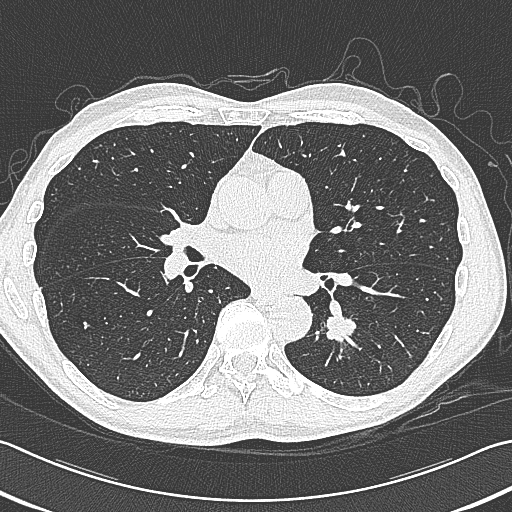
Chest CT (low-dose screening protocol), one axial image. First (baseline) screen. Lung window (W 1500 / L -600 HU). 1 mm slice thickness. Lung (sharp) reconstruction kernel (B80f). 120 kVp. Male participant, aged 59 years at enrolment.
Expert-annotated lung lesion, bounding box <313,295,376,353> (left, top, right, bottom; pixels). Reader record for this screening exam (exam-level; its link to the box is not recorded): non-calcified nodule or mass ≥4 mm, left lower lobe, 15 × 15 mm, smooth margins, soft tissue attenuation. Official screen result: positive, change unspecified: nodule(s) >= 4 mm or enlarging nodule(s), mass(es), or other non-specific abnormalities suspicious for lung cancer. Participant outcome: lung cancer diagnosed 17 days after this screen — squamous cell carcinoma, large cell, nonkeratinizing, NOS, left lower lobe, poorly differentiated (G3), stage IB (AJCC 6th edition), 31 mm at pathology.